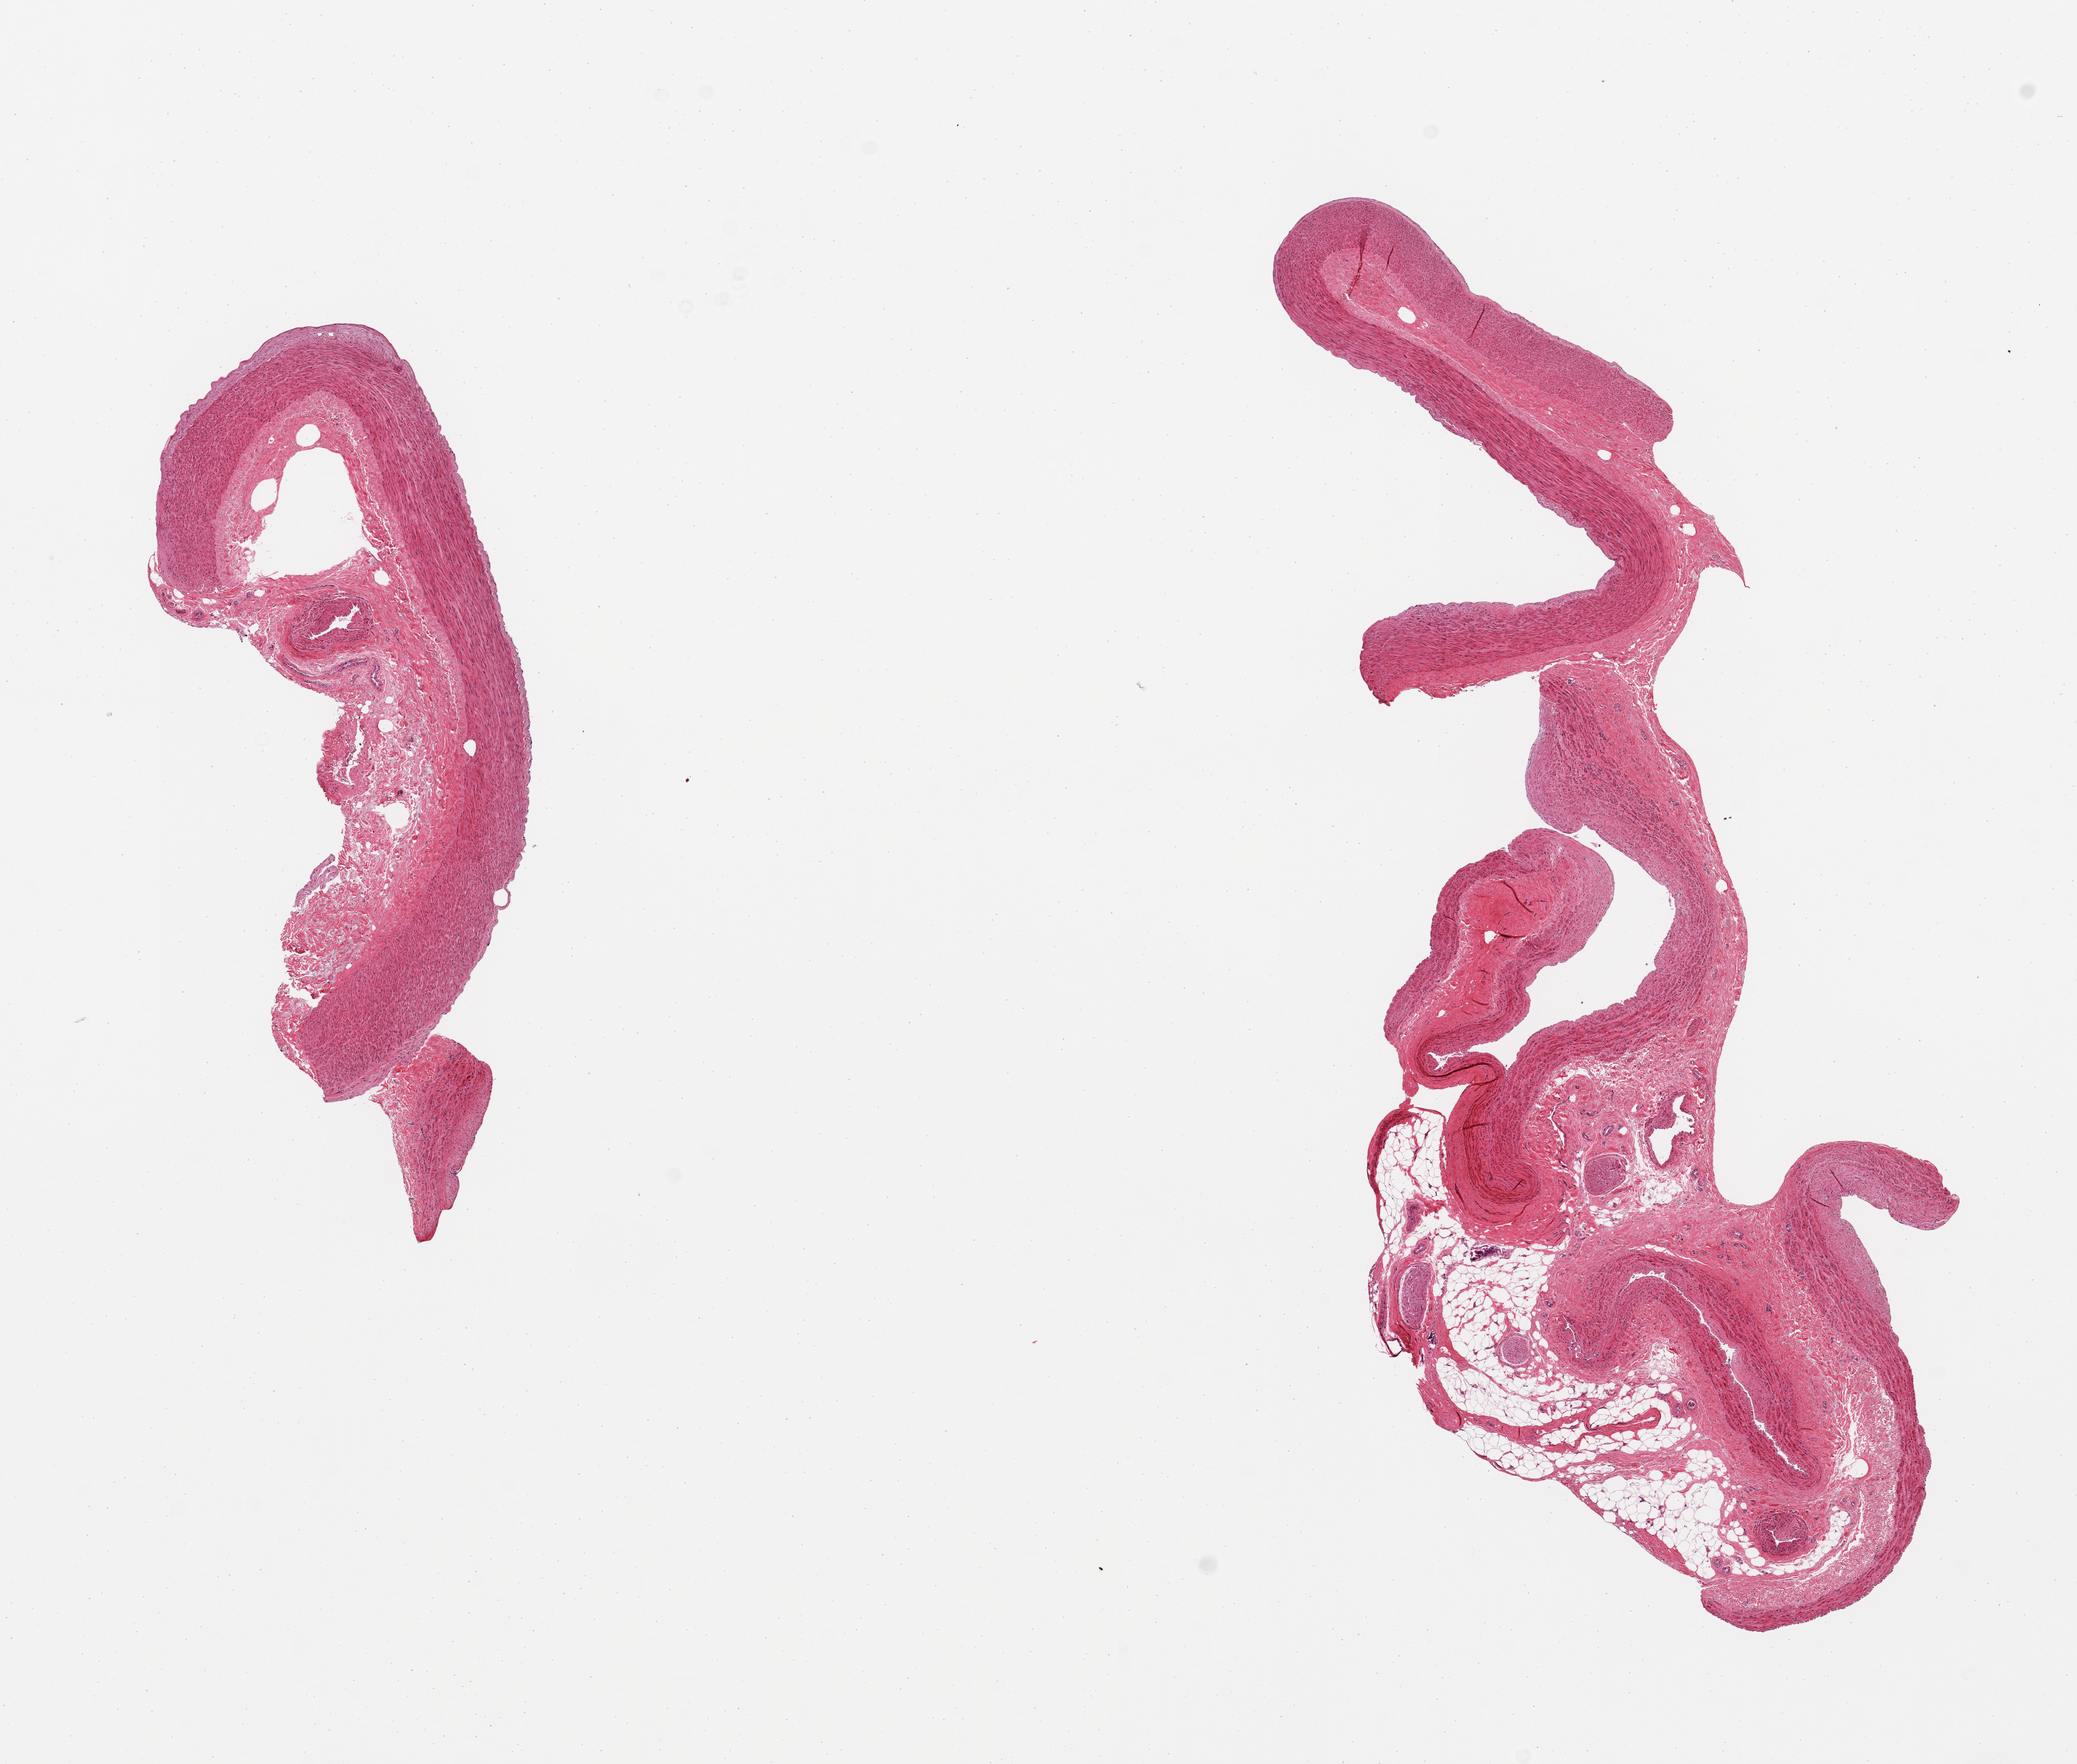
Hematoxylin and eosin (H&E) whole-slide image, brightfield — shown as a low-resolution overview of the whole scanned area (about 12.8 x 10.9 mm, acquisition: 20x scan). PAXgene-fixed paraffin-embedded (PFPE) section. Target tissue: tibial artery. Tissue donor sample. Donor: male.
Pathologist's review note for this sample: 2 pieces; up to 40% perivascularstroma.